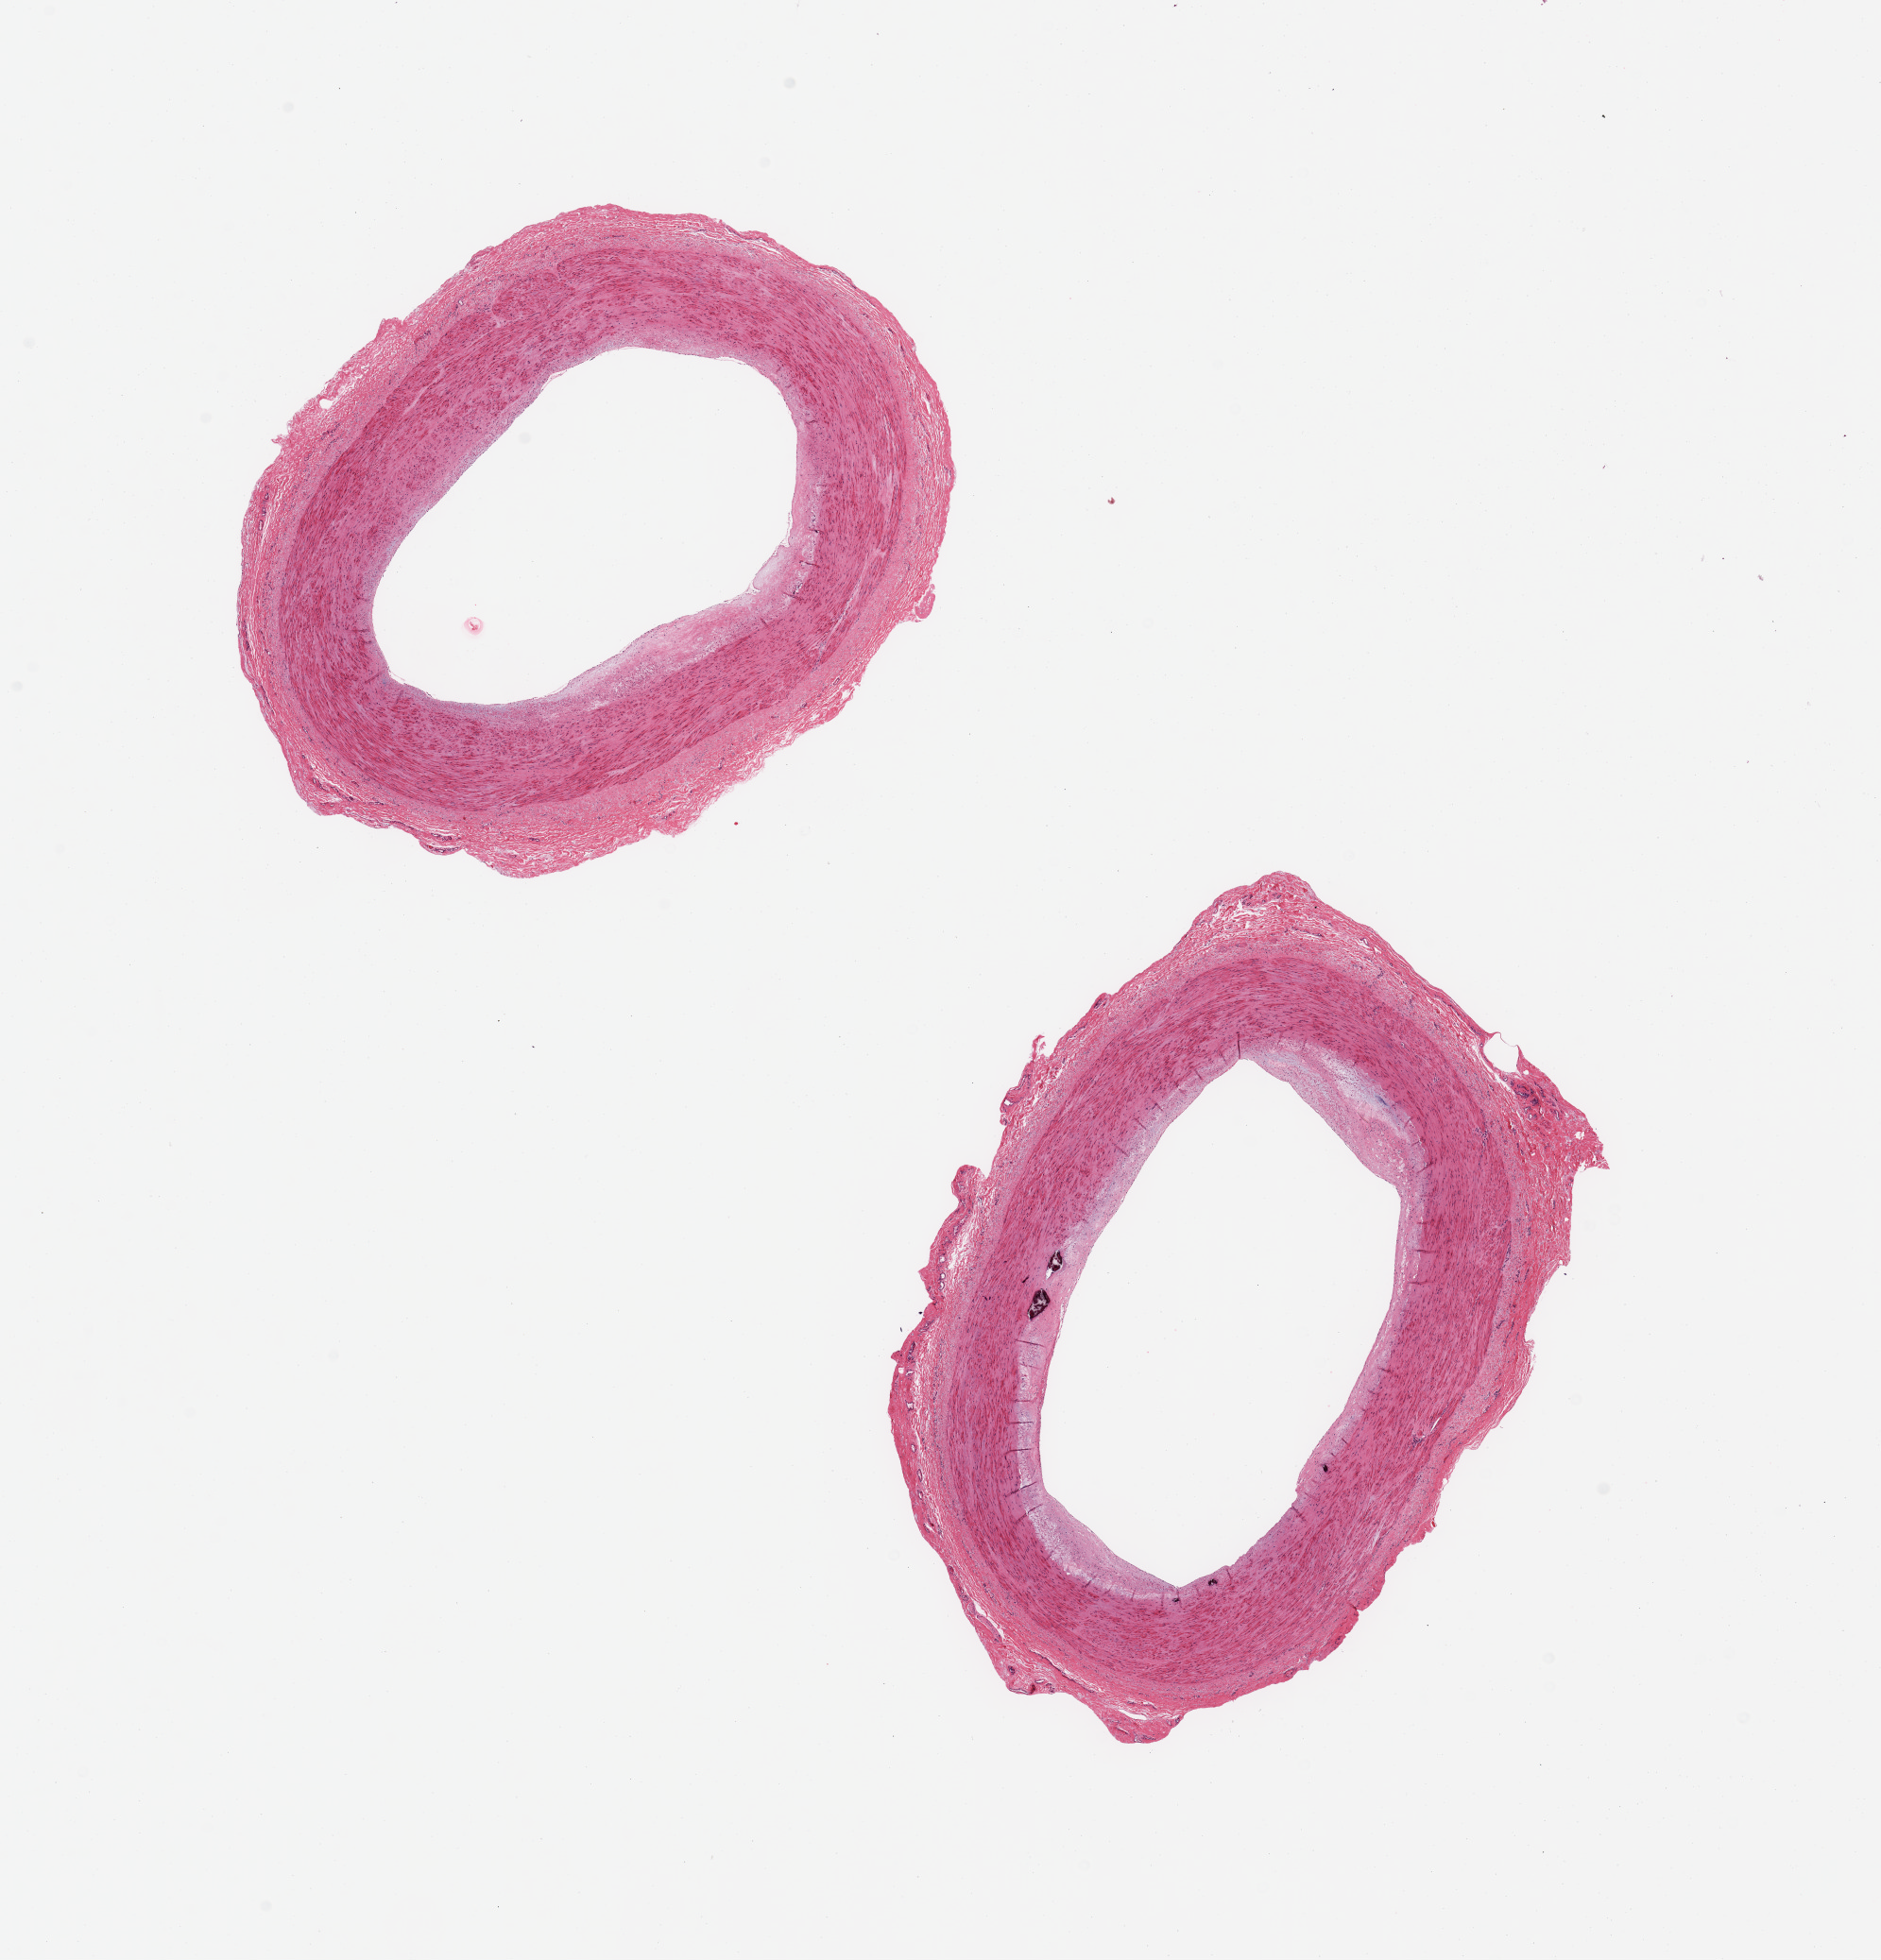
Digitized hematoxylin and eosin (H&E)-stained section, brightfield, low-resolution overview of the scanned area, about 15.8 x 16.4 mm (from a 20x scan). PAXgene-fixed paraffin-embedded (PFPE) section. Target tissue: tibial artery. Tissue donor sample.
* reviewer comment on this tissue sample: 2 pieces; fibrosclerotic plaque; medial discrete calcifications; lumina open with ~25% narrowing; attached rim of adventitia